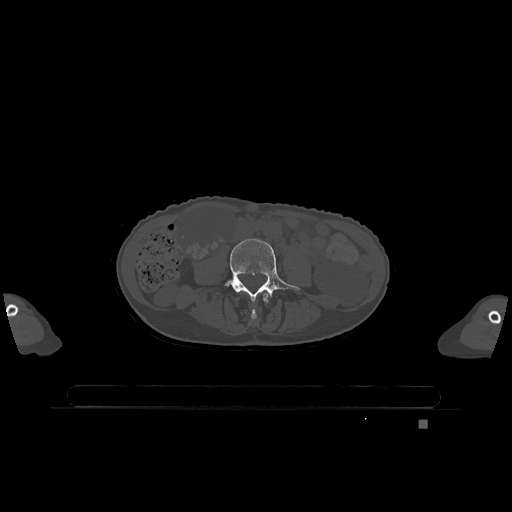
CT including the spine, one axial slice. Bone window (W 1800 / L 400 HU). 0.5 mm slice thickness. 512 × 512 image matrix, field of view 500 × 500 mm. Patient: female, 74 years. Case-level facts recorded for this patient, not image findings: primary cancer: lung.
Annotated regions visible in this slice (semi-automatically segmented with operator editing):
- L3 vertebra: bounding box (x1, y1, x2, y2) in pixels: (251, 292, 270, 320)
- L4 vertebra: (224, 239, 300, 301)